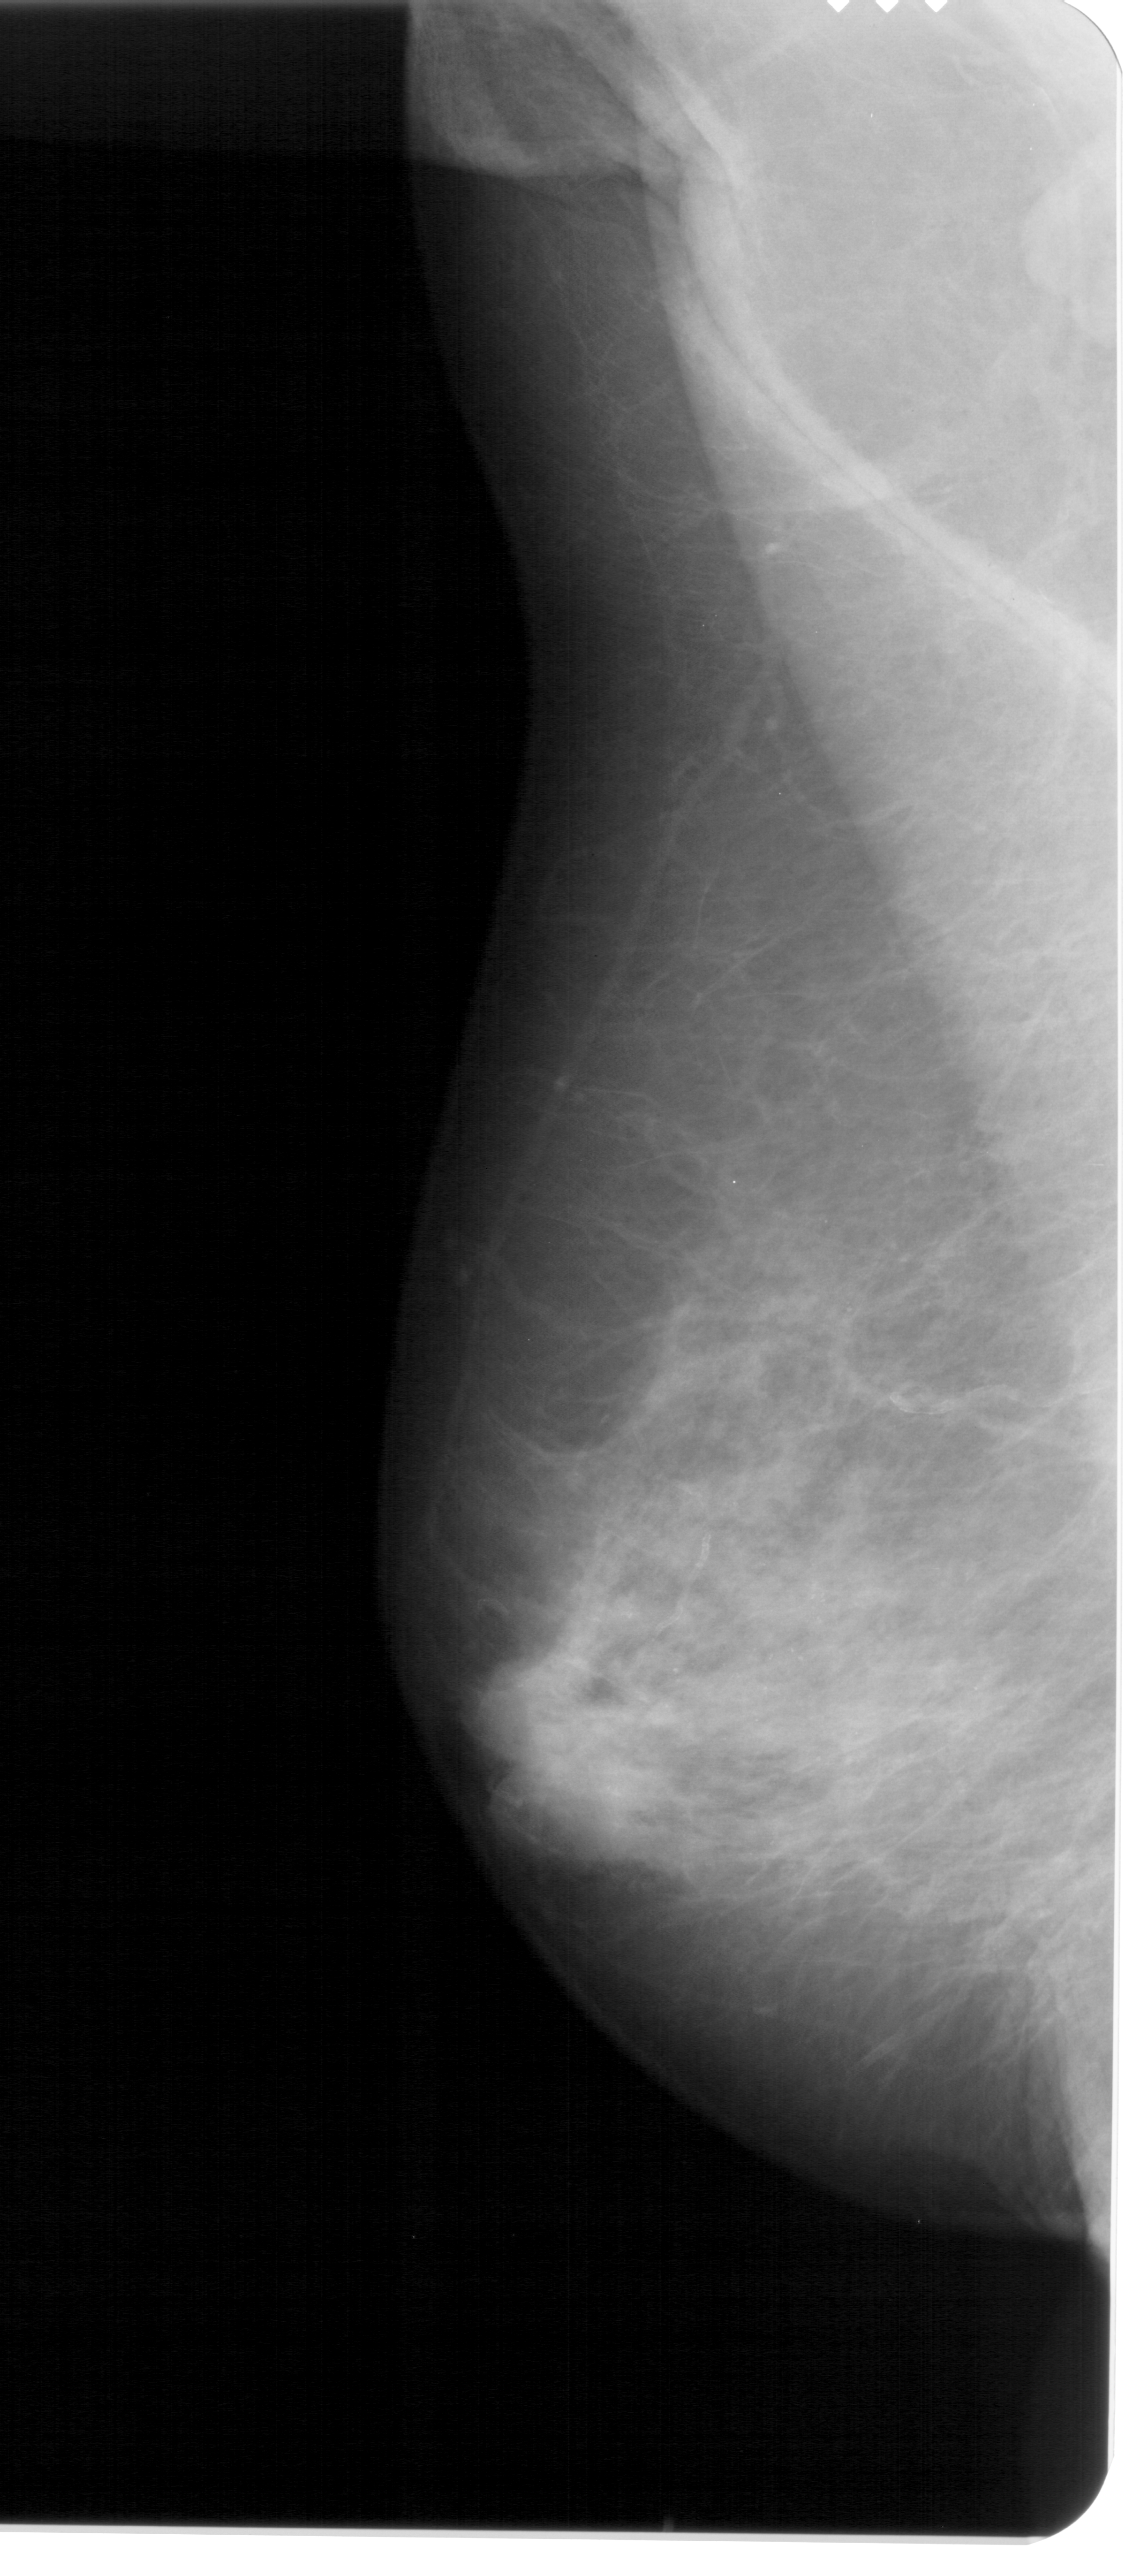
Mammogram (digitized film), left breast, mediolateral oblique (MLO) view, BI-RADS breast density category 4 (scale 1–4).
- Marked findings (only marked abnormalities are described; nothing is implied about the rest of the image): calcifications, morphology punctate / amorphous, distribution regional; BI-RADS assessment category 4; subtlety rating 3 on a 1 (subtle) to 5 (obvious) scale; pathology (as recorded): benign.